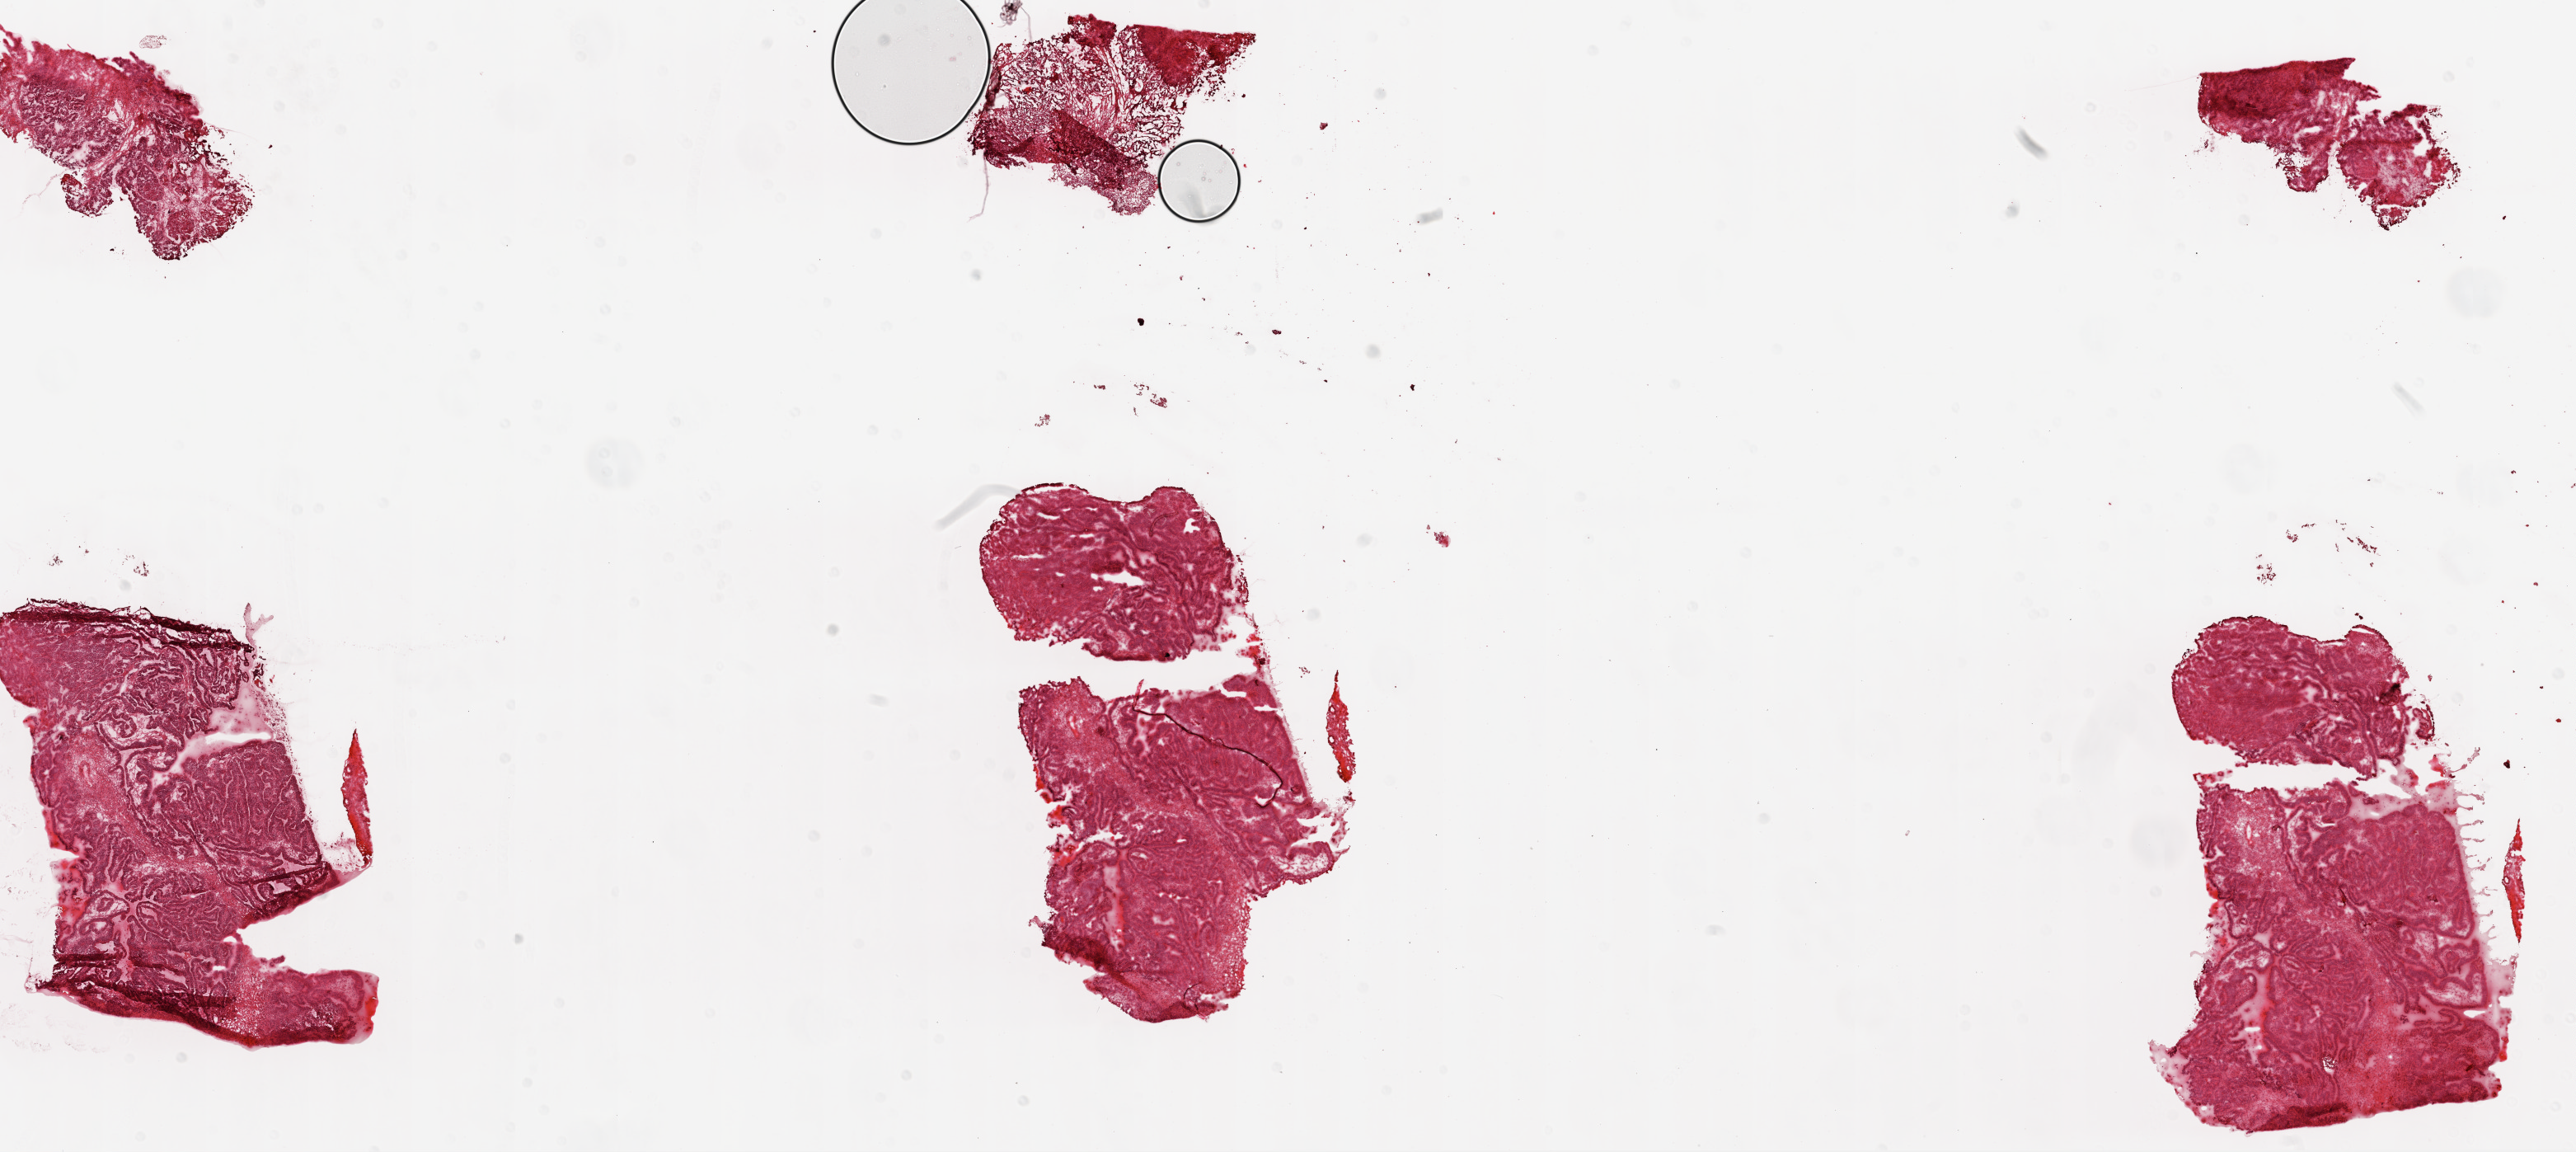
Digitized H&E tissue section (whole slide), low-resolution overview of the scanned area, about 25.1 x 11.2 mm (from a 20x scan). Frozen section. Ovary, primary tumour sample. Patient: female, age at initial diagnosis 54 years. Histologic grade: G3 (poorly differentiated). Pathologist review of this section (percent, as recorded): tumour cells 95%, tumour nuclei 95%, normal cells 0%, stromal cells 5%, necrosis 0%.
- FIGO stage: IIIB
- diagnosis: Serous cystadenocarcinoma, NOS